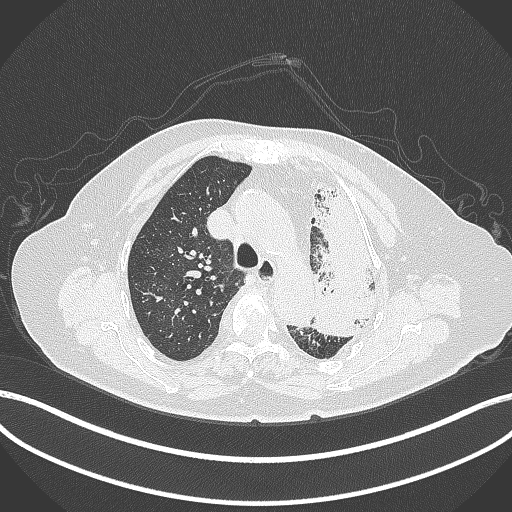
Chest CT, one axial slice. Reconstruction kernel B70f. 120 kVp. Lung window (W 1500 / L -600 HU). 1 mm slice thickness. 512 × 512 image matrix. Female patient, age 75 years. From the clinical record (not read from this slice): clinical TNM (as recorded): T3 N3 M1.
Annotated regions visible in this slice (bounding box drawn by a radiologist):
- lung tumour (recorded histology: adenocarcinoma): box from (x=303, y=182) to (x=382, y=339) px